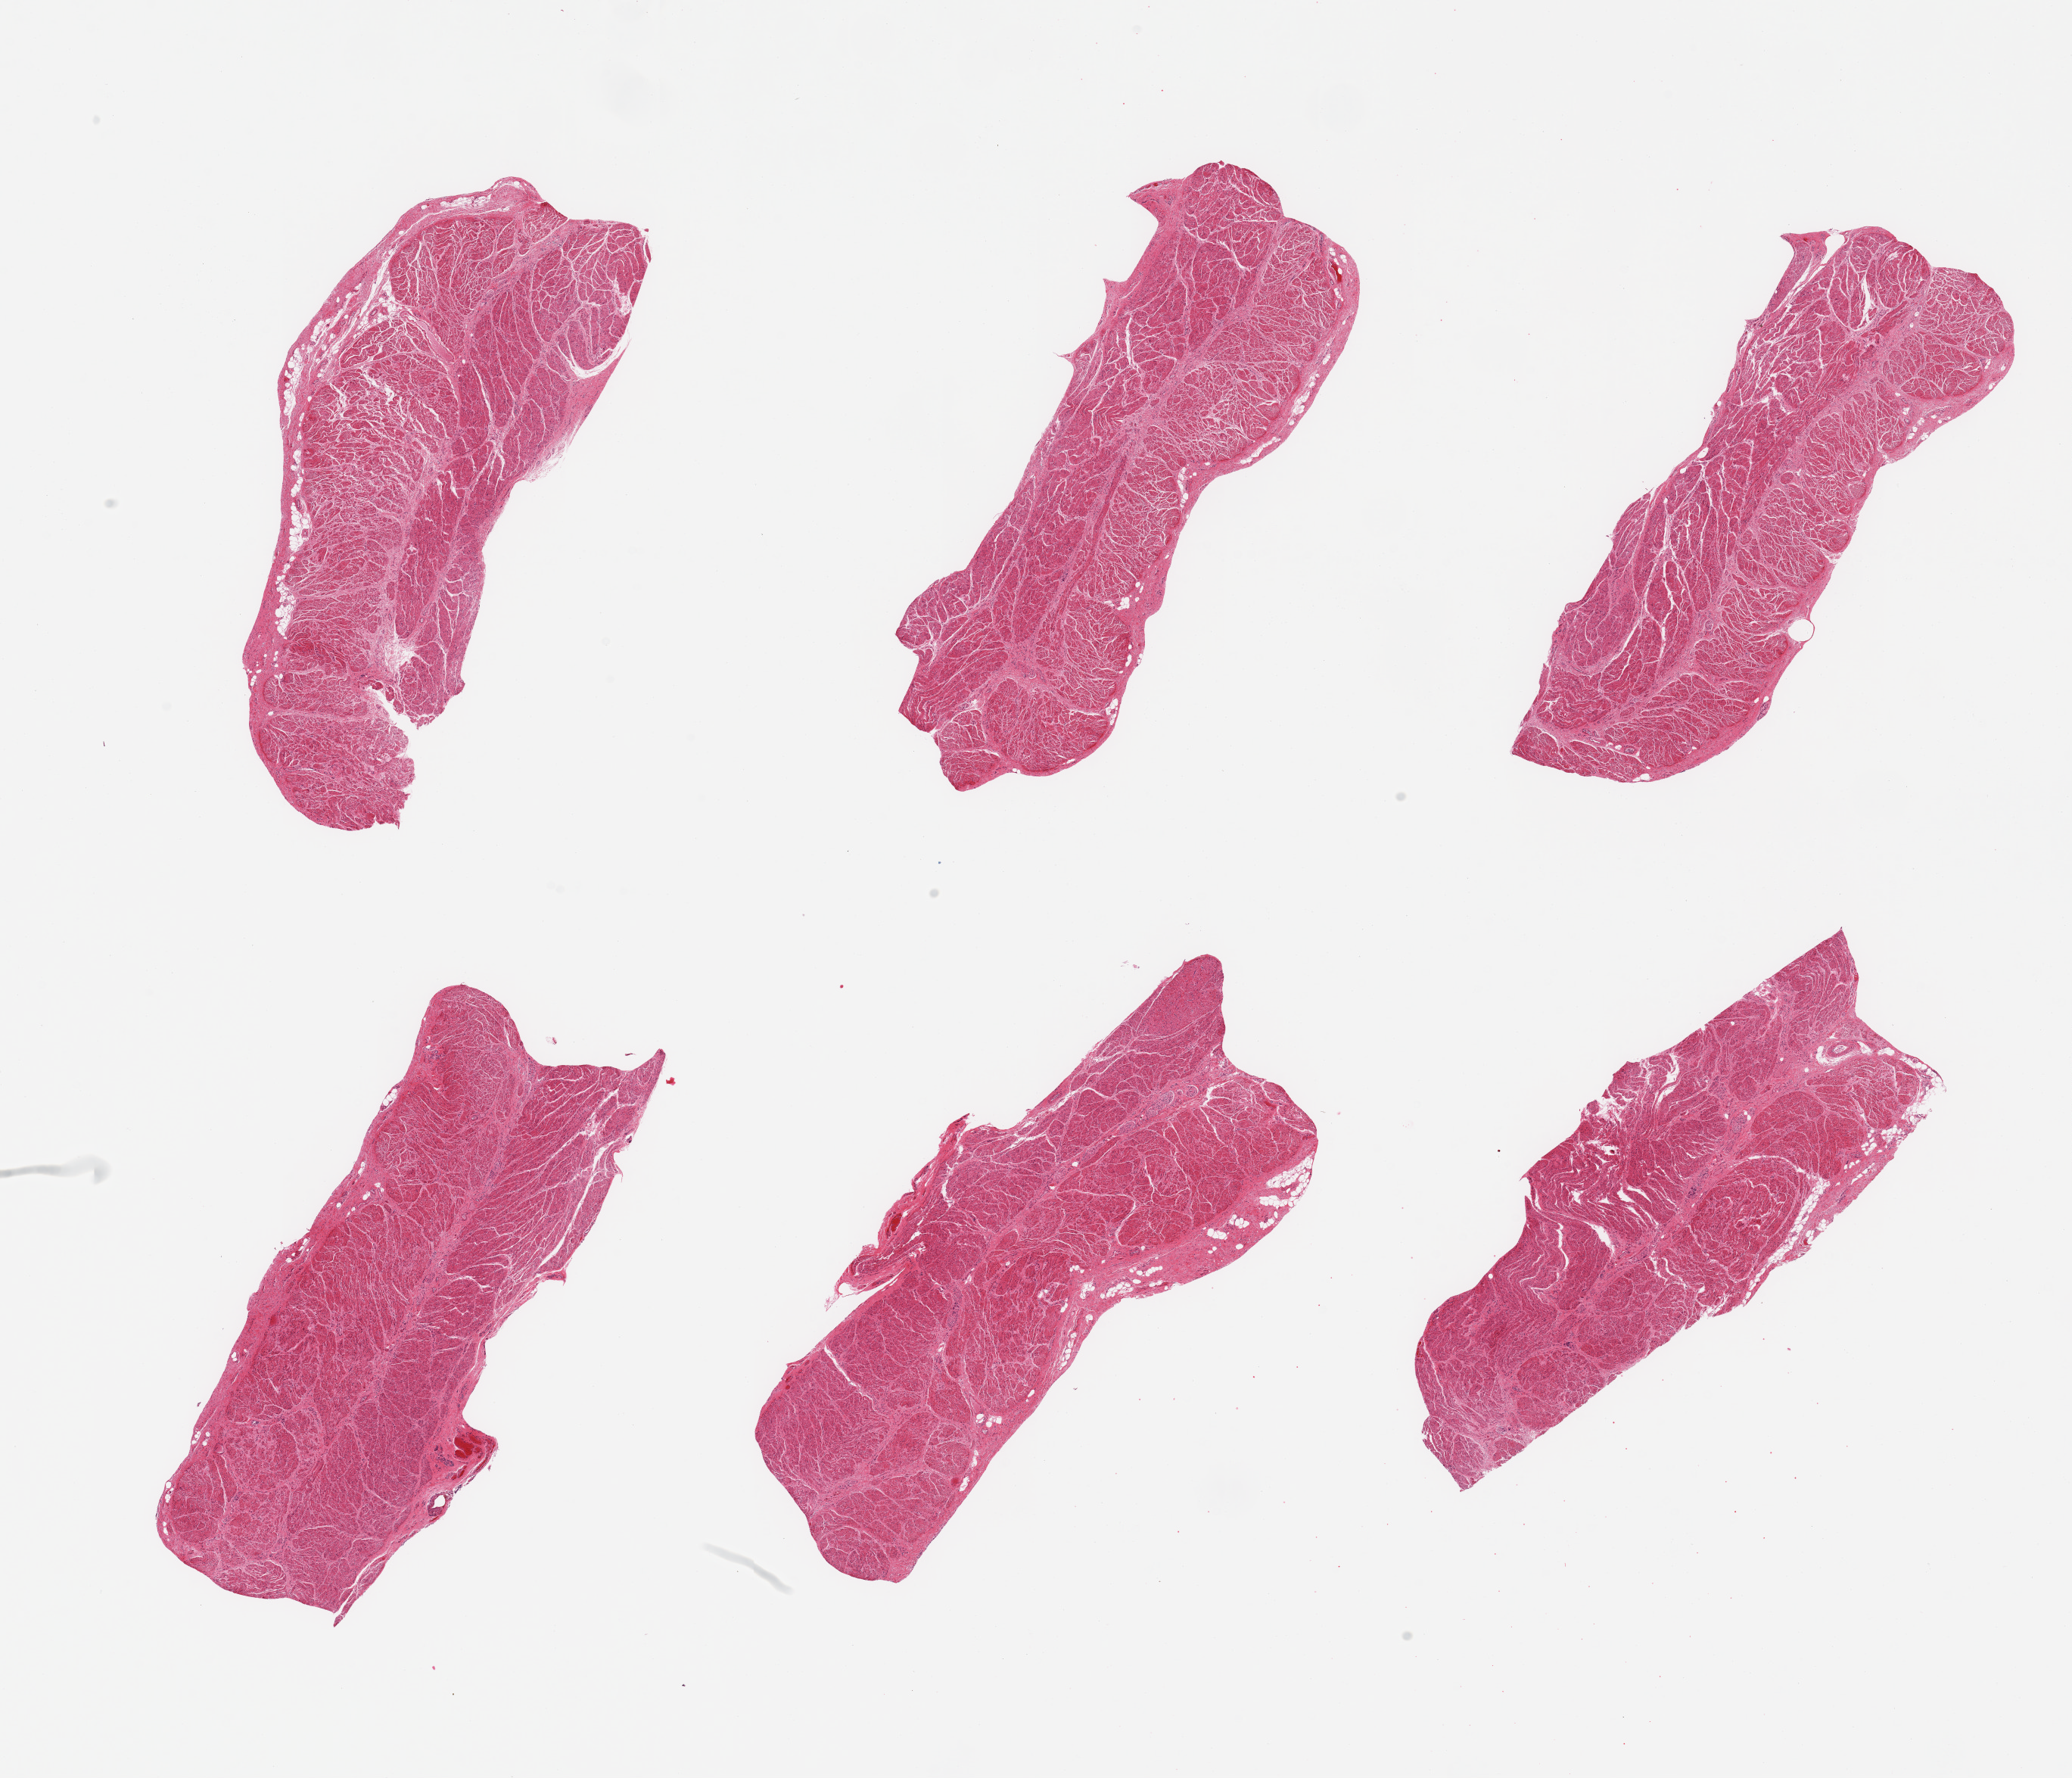
Whole-slide image, haematoxylin and eosin stain, a low-resolution overview of the entire scanned area, about 21.7 x 18.6 mm (from a 20x scan), PAXgene-fixed paraffin-embedded (PFPE) section, sampled site (target tissue): gastroesophageal junction, tissue donor sample. Male donor.
- reviewer comment on this tissue sample: 6 pieces, confirmed target muscularis